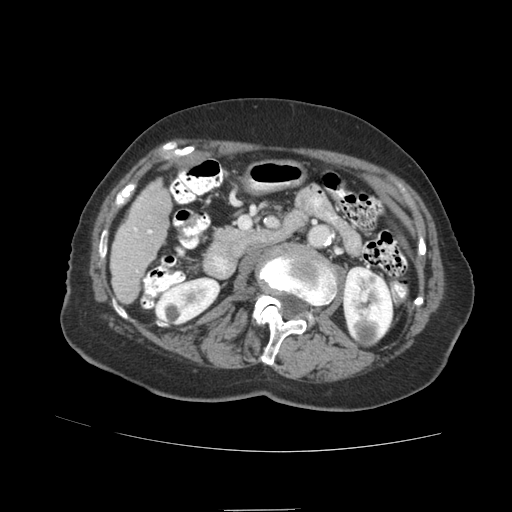
Contrast-enhanced abdominal CT (liver protocol), one axial slice; reconstruction kernel STANDARD; soft-tissue window (W 400 / L 40 HU); 2.5 mm slice thickness; 512 × 512 image matrix. From the clinical record (not read from this slice): diagnosis: hepatocellular carcinoma (patient treated with transarterial chemoembolisation; whether this scan precedes or follows treatment is not stated here); TNM stage (as recorded): Stage-II; Child-Pugh class: A; tumour differentiation: moderately differentiated.
Outlined on this slice (semi-automatic segmentation, software-assisted and operator-edited):
- liver parenchyma outside the tumour (the mass and vessels are separate outlines, so this box may not span the whole liver): box from (x=110, y=180) to (x=172, y=304) px
- liver vessels: (x=134, y=204)–(x=152, y=272)